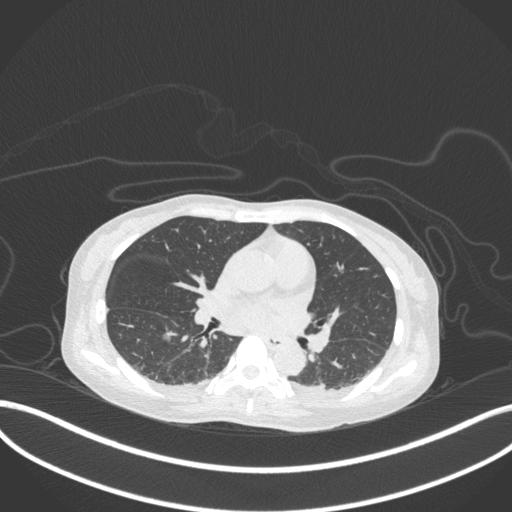
Chest CT, one axial slice; position 160 of 260 along the scan axis; reconstruction kernel B31f; 120 kVp; lung window (W 1500 / L -600 HU); 1 mm slice thickness; 512 × 512 image matrix, field of view 400 × 400 mm. Patient: female, 44 years. Case-level facts recorded for this patient, not image findings: clinical TNM (as recorded): T1c N0 M0.
Outlined on this slice (bounding box drawn by a radiologist):
- lung tumour (recorded histology: adenocarcinoma): bounding box (x1, y1, x2, y2) in pixels: (159, 326, 181, 346)